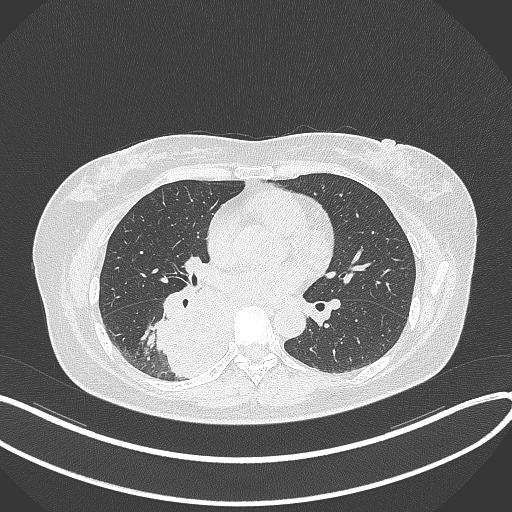
Chest CT, one axial slice; slice 175 of 331 in the series (ordered by position); 120 kVp; lung window (W 1500 / L -600 HU); 1 mm slice thickness; 512 × 512 image matrix, field of view 400 × 400 mm. Female patient, age 54 years. Case-level facts recorded for this patient, not image findings: clinical TNM (as recorded): T4 N0 M0.
Outlined on this slice (bounding box drawn by a radiologist):
- lung tumour (recorded histology: adenocarcinoma): box from (x=151, y=280) to (x=233, y=382) px